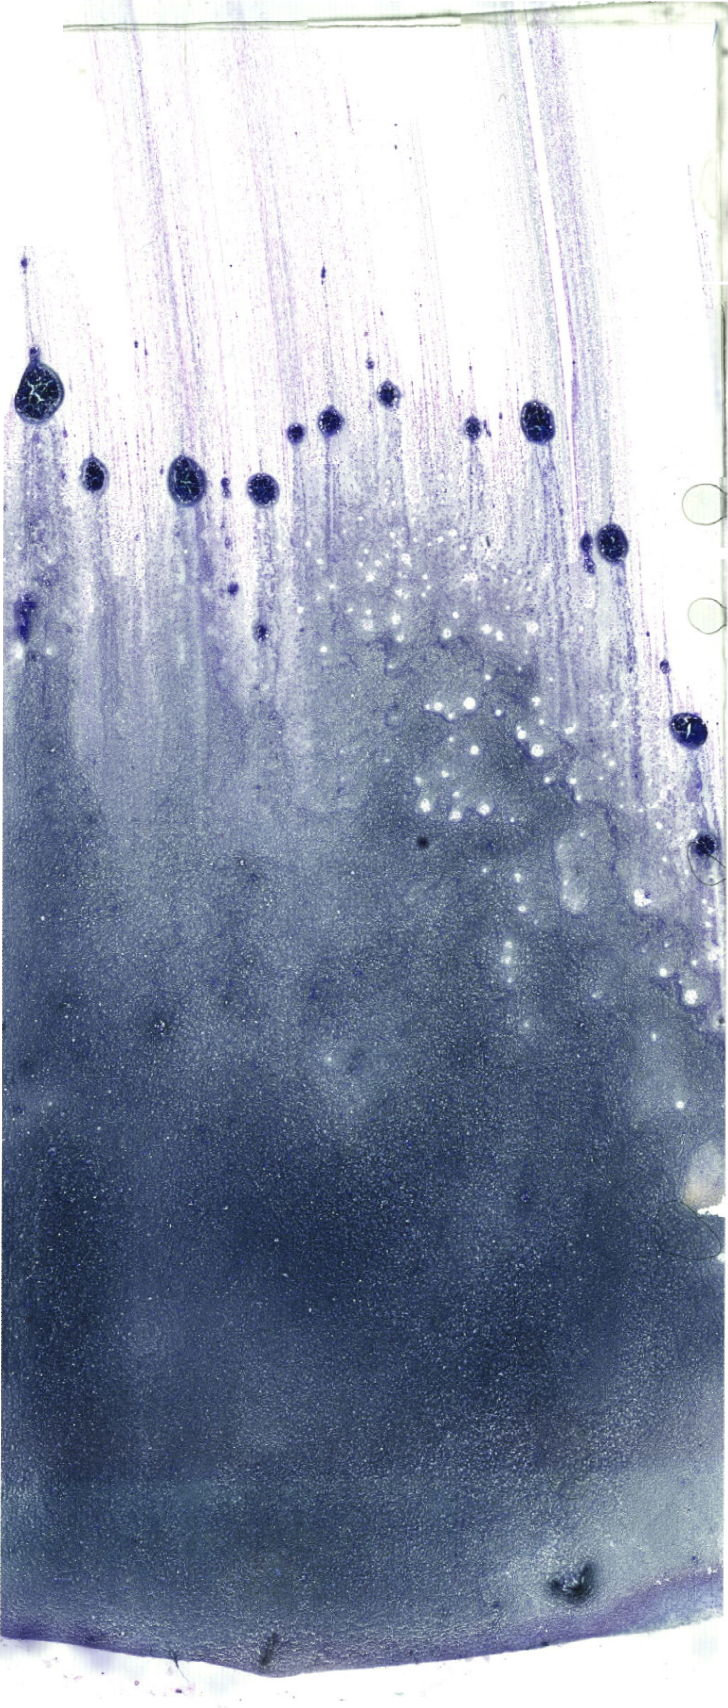
Bone marrow aspirate smear, May-Grünwald–Giemsa stain, whole-slide image — a low-resolution overview of the entire scanned area, about 20.6 x 48.4 mm.
Diagnosis: Burkitt Leukemia.